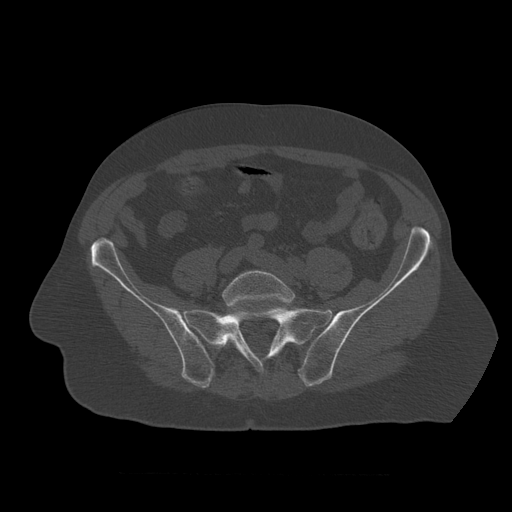
CT including the spine, one axial slice. Slice 242 of 450 in the series (ordered by position). 120 kVp. Bone window (W 1800 / L 400 HU). 512 × 512 image matrix, field of view 405 × 405 mm. Patient age 75 years. Case-level facts recorded for this patient, not image findings: primary cancer: prostate.
Outlined on this slice (semi-automatic segmentation, software-assisted and operator-edited):
- L5 vertebra: bounding box [x1, y1, x2, y2] px = [222, 270, 296, 307]